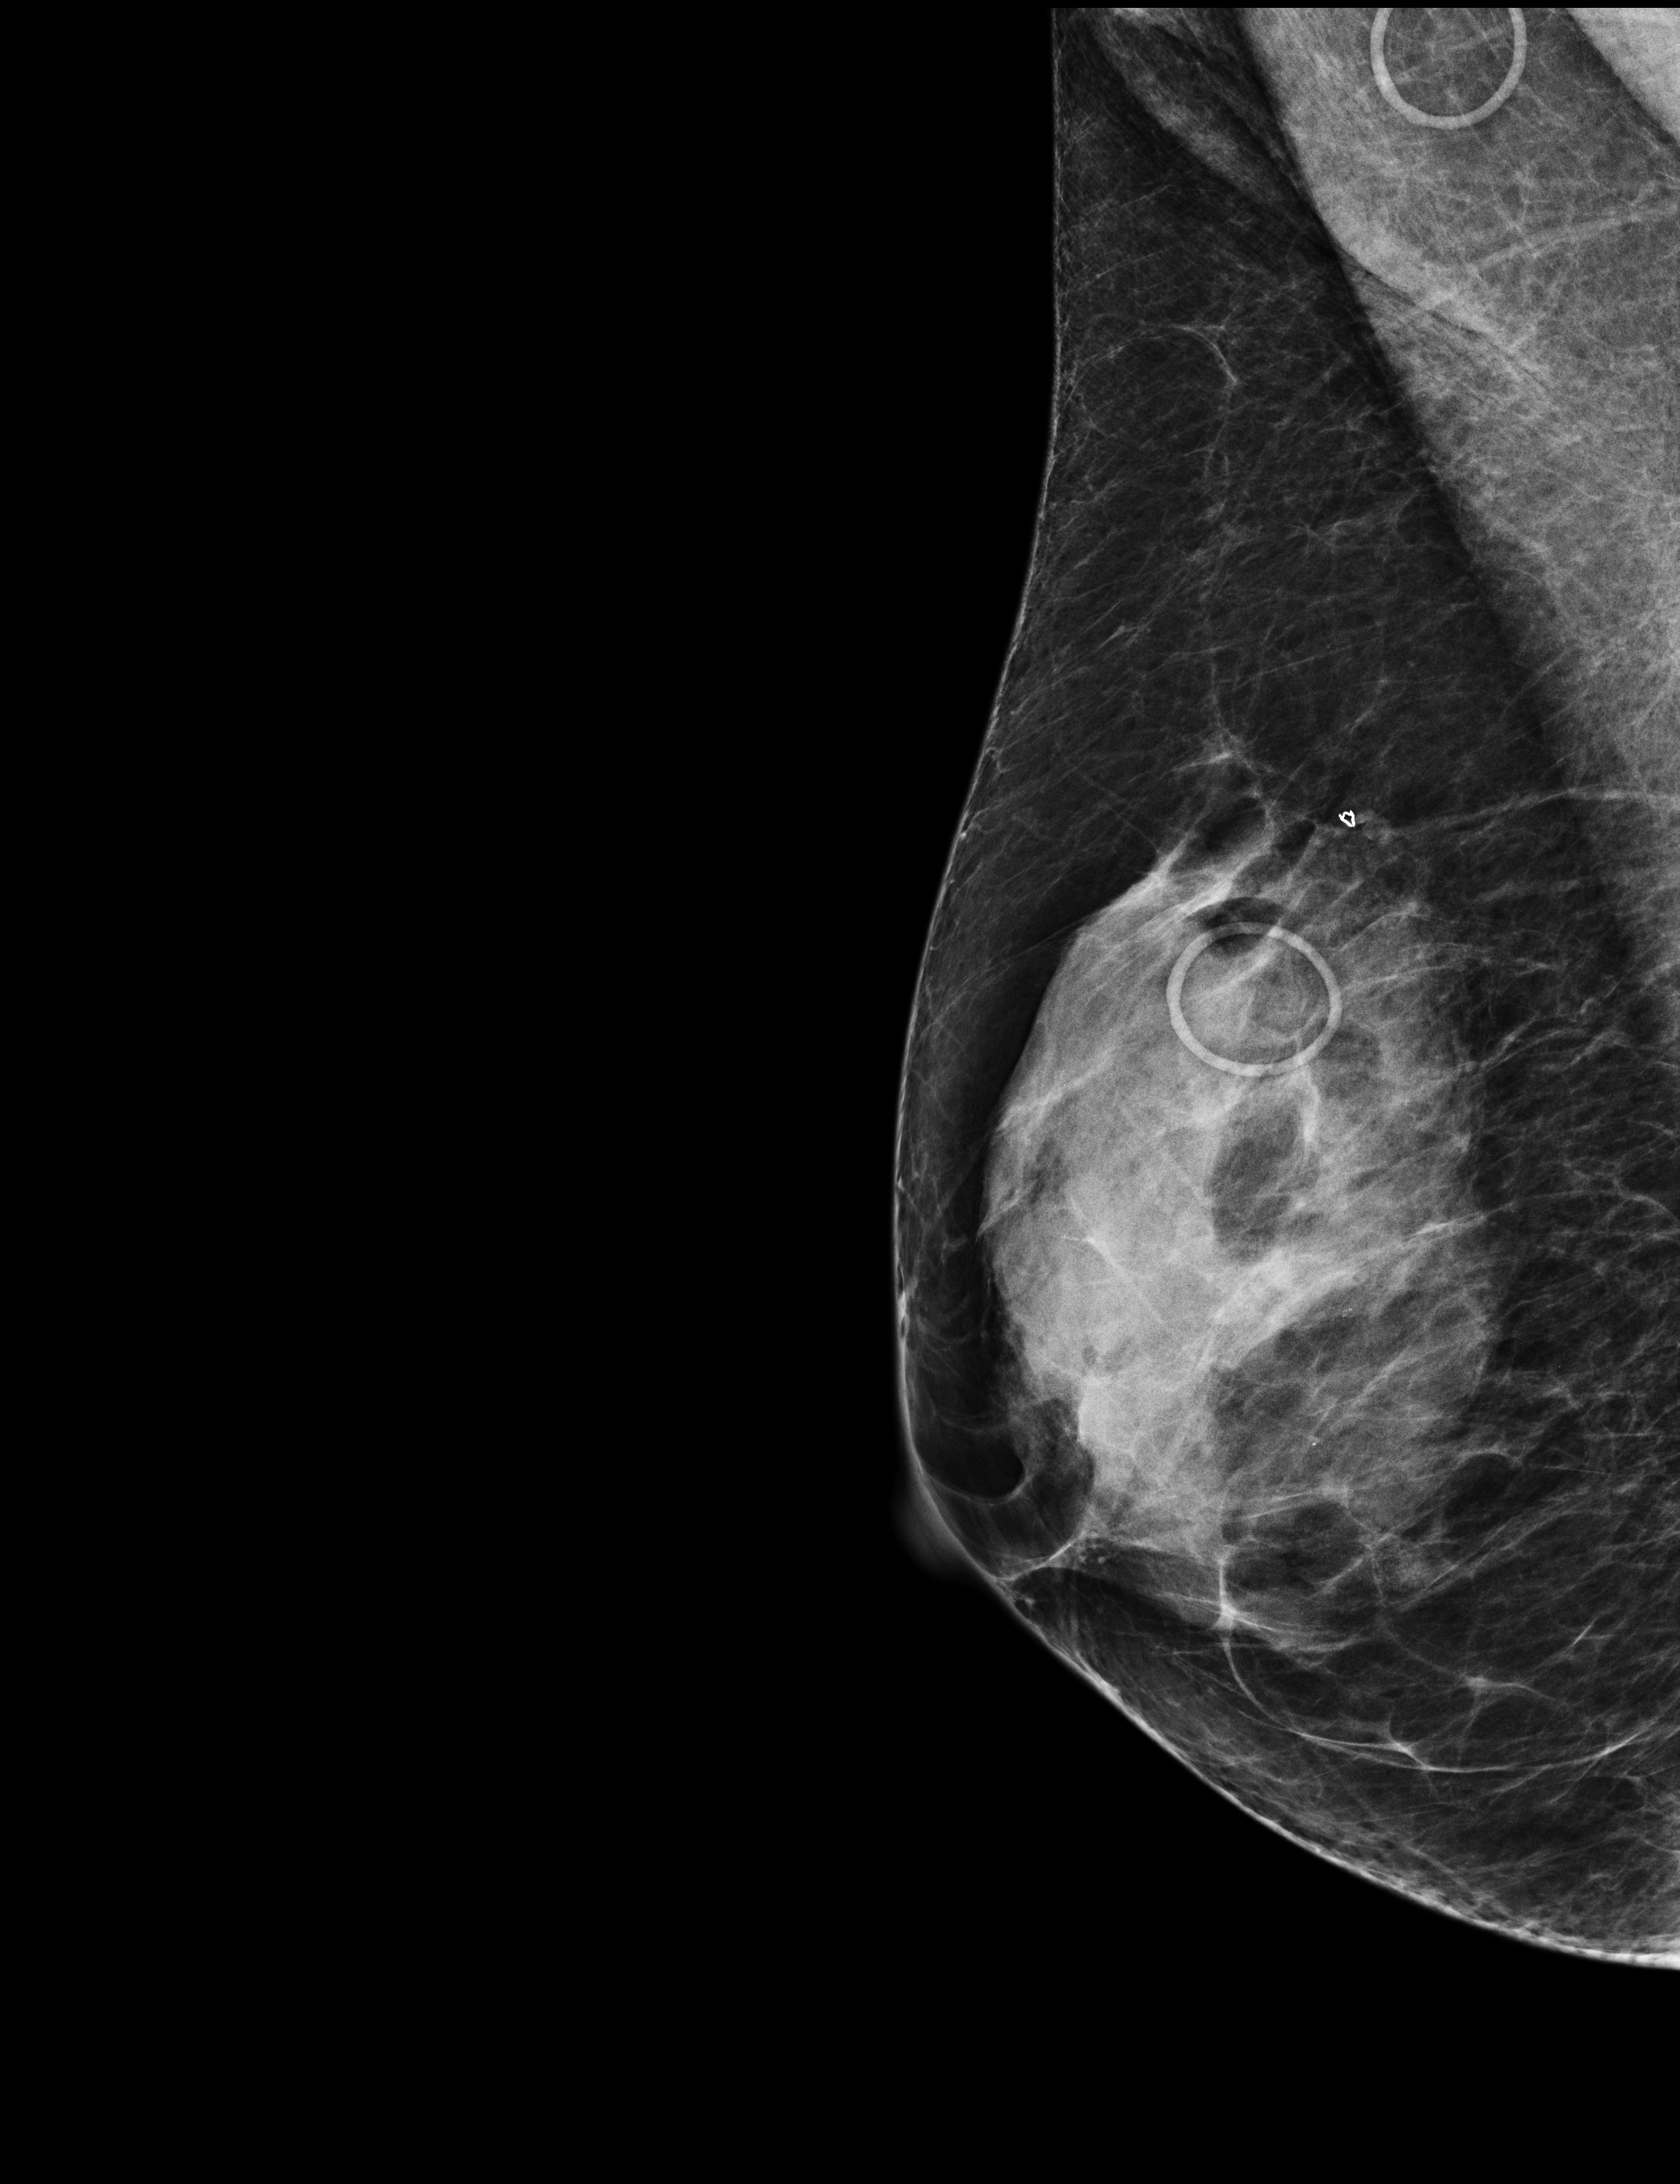
Full-field digital mammogram (FFDM), right breast, mediolateral oblique (MLO) view, annual screening mammography examination, compressed breast thickness 50 mm. Patient aged 66 years (female).
Breast density at the screening exam (both breasts): heterogeneously dense (BI-RADS density category c). Final BI-RADS category for the screening round (tomosynthesis exam, both breasts): category 1. Recall: no recall after this screen.